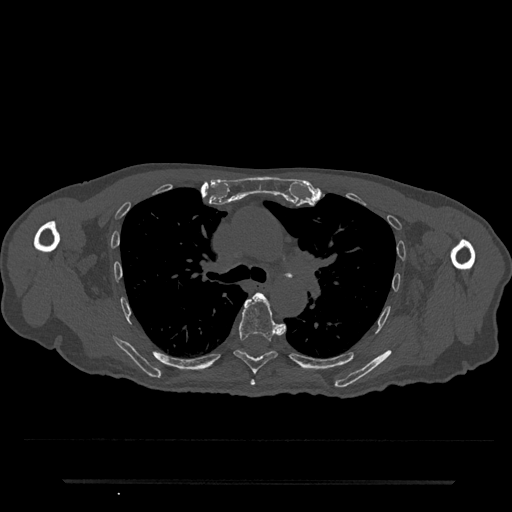
CT including the spine, one axial slice. Slice 529 of 797 in the series (ordered by position). Bone window (W 1800 / L 400 HU). 0.5 mm slice thickness. 512 × 512 image matrix, field of view 427 × 427 mm. Male patient, age 74 years. Case-level facts recorded for this patient, not image findings: primary cancer: prostate.
Structures marked on this image (semi-automatically segmented with operator editing):
- T5 vertebra: bounding box (x1, y1, x2, y2) in pixels: (250, 380, 255, 386)
- T6 vertebra: (234, 293, 283, 374)